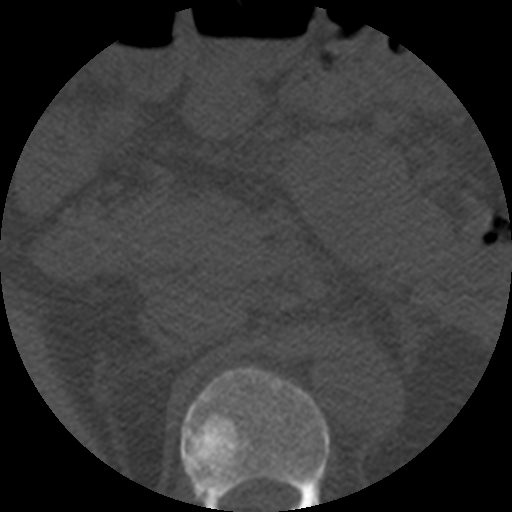
CT including the spine, one axial slice. Position 223 of 508 along the scan axis. Reconstruction kernel STANDARD. Bone window (W 1800 / L 400 HU). 1.25 mm slice thickness. 512 × 512 image matrix, field of view 160 × 160 mm. Patient age 57 years. From the clinical record (not read from this slice): primary cancer: prostate.
Annotated regions visible in this slice (semi-automatic segmentation, software-assisted and operator-edited):
- T12 vertebra: bounding box (x1, y1, x2, y2) in pixels: (180, 367, 330, 512)